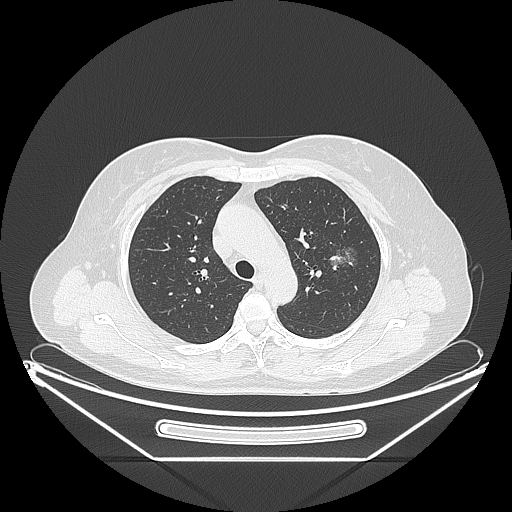
Chest CT, one axial slice; position 155 of 226 along the scan axis; reconstruction kernel LUNG; 120 kVp; lung window (W 1500 / L -600 HU); 512 × 512 image matrix. Female patient, age 54 years. From the clinical record (not read from this slice): clinical TNM (as recorded): T1c N0 M0; histopathological grade: G1.
Annotated regions visible in this slice (rectangle marked by the reading radiologist):
- lung tumour (recorded histology: adenocarcinoma): box from (x=328, y=238) to (x=360, y=276) px